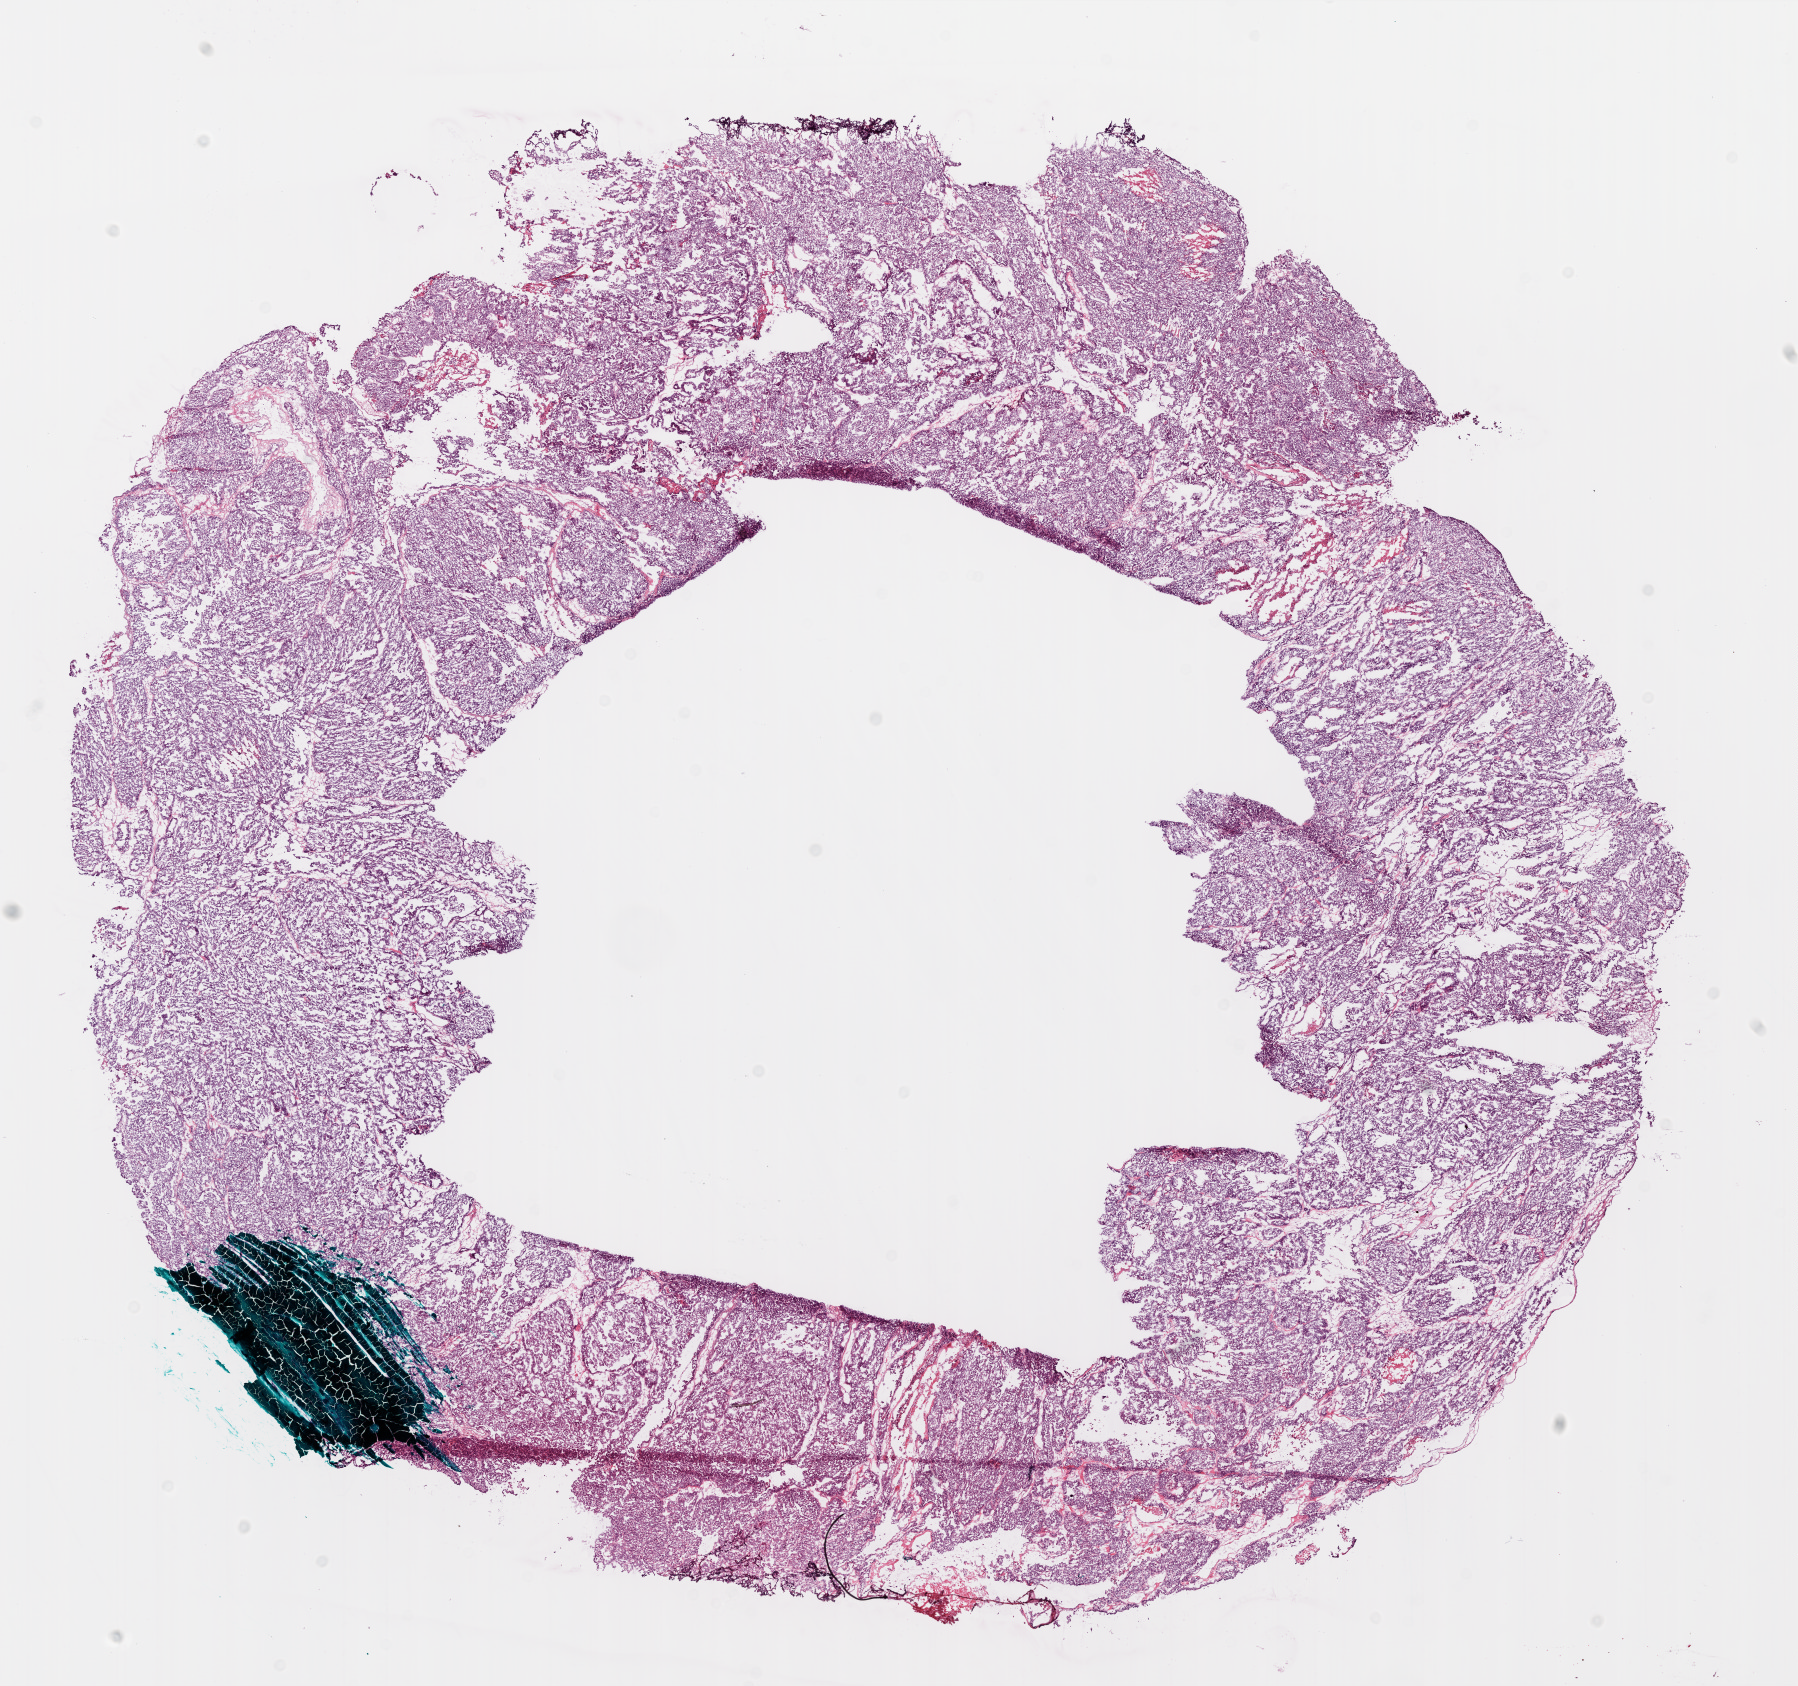
Whole-slide histology image, H&E — a low-resolution overview of the entire scanned area, about 14.5 x 13.6 mm (acquisition: 20x scan). Frozen section from the bottom of the tissue portion. Ovary, primary tumour sample. Female, age 60 years at initial diagnosis. Histologic grade: G3 (poorly differentiated). Slide review estimates, as recorded: tumour cells 92%, tumour nuclei 98%, normal cells 0%, stromal cells 8%, necrosis 0%.
Diagnosis: Serous cystadenocarcinoma, NOS. Laterality: bilateral. FIGO stage: IIIC.